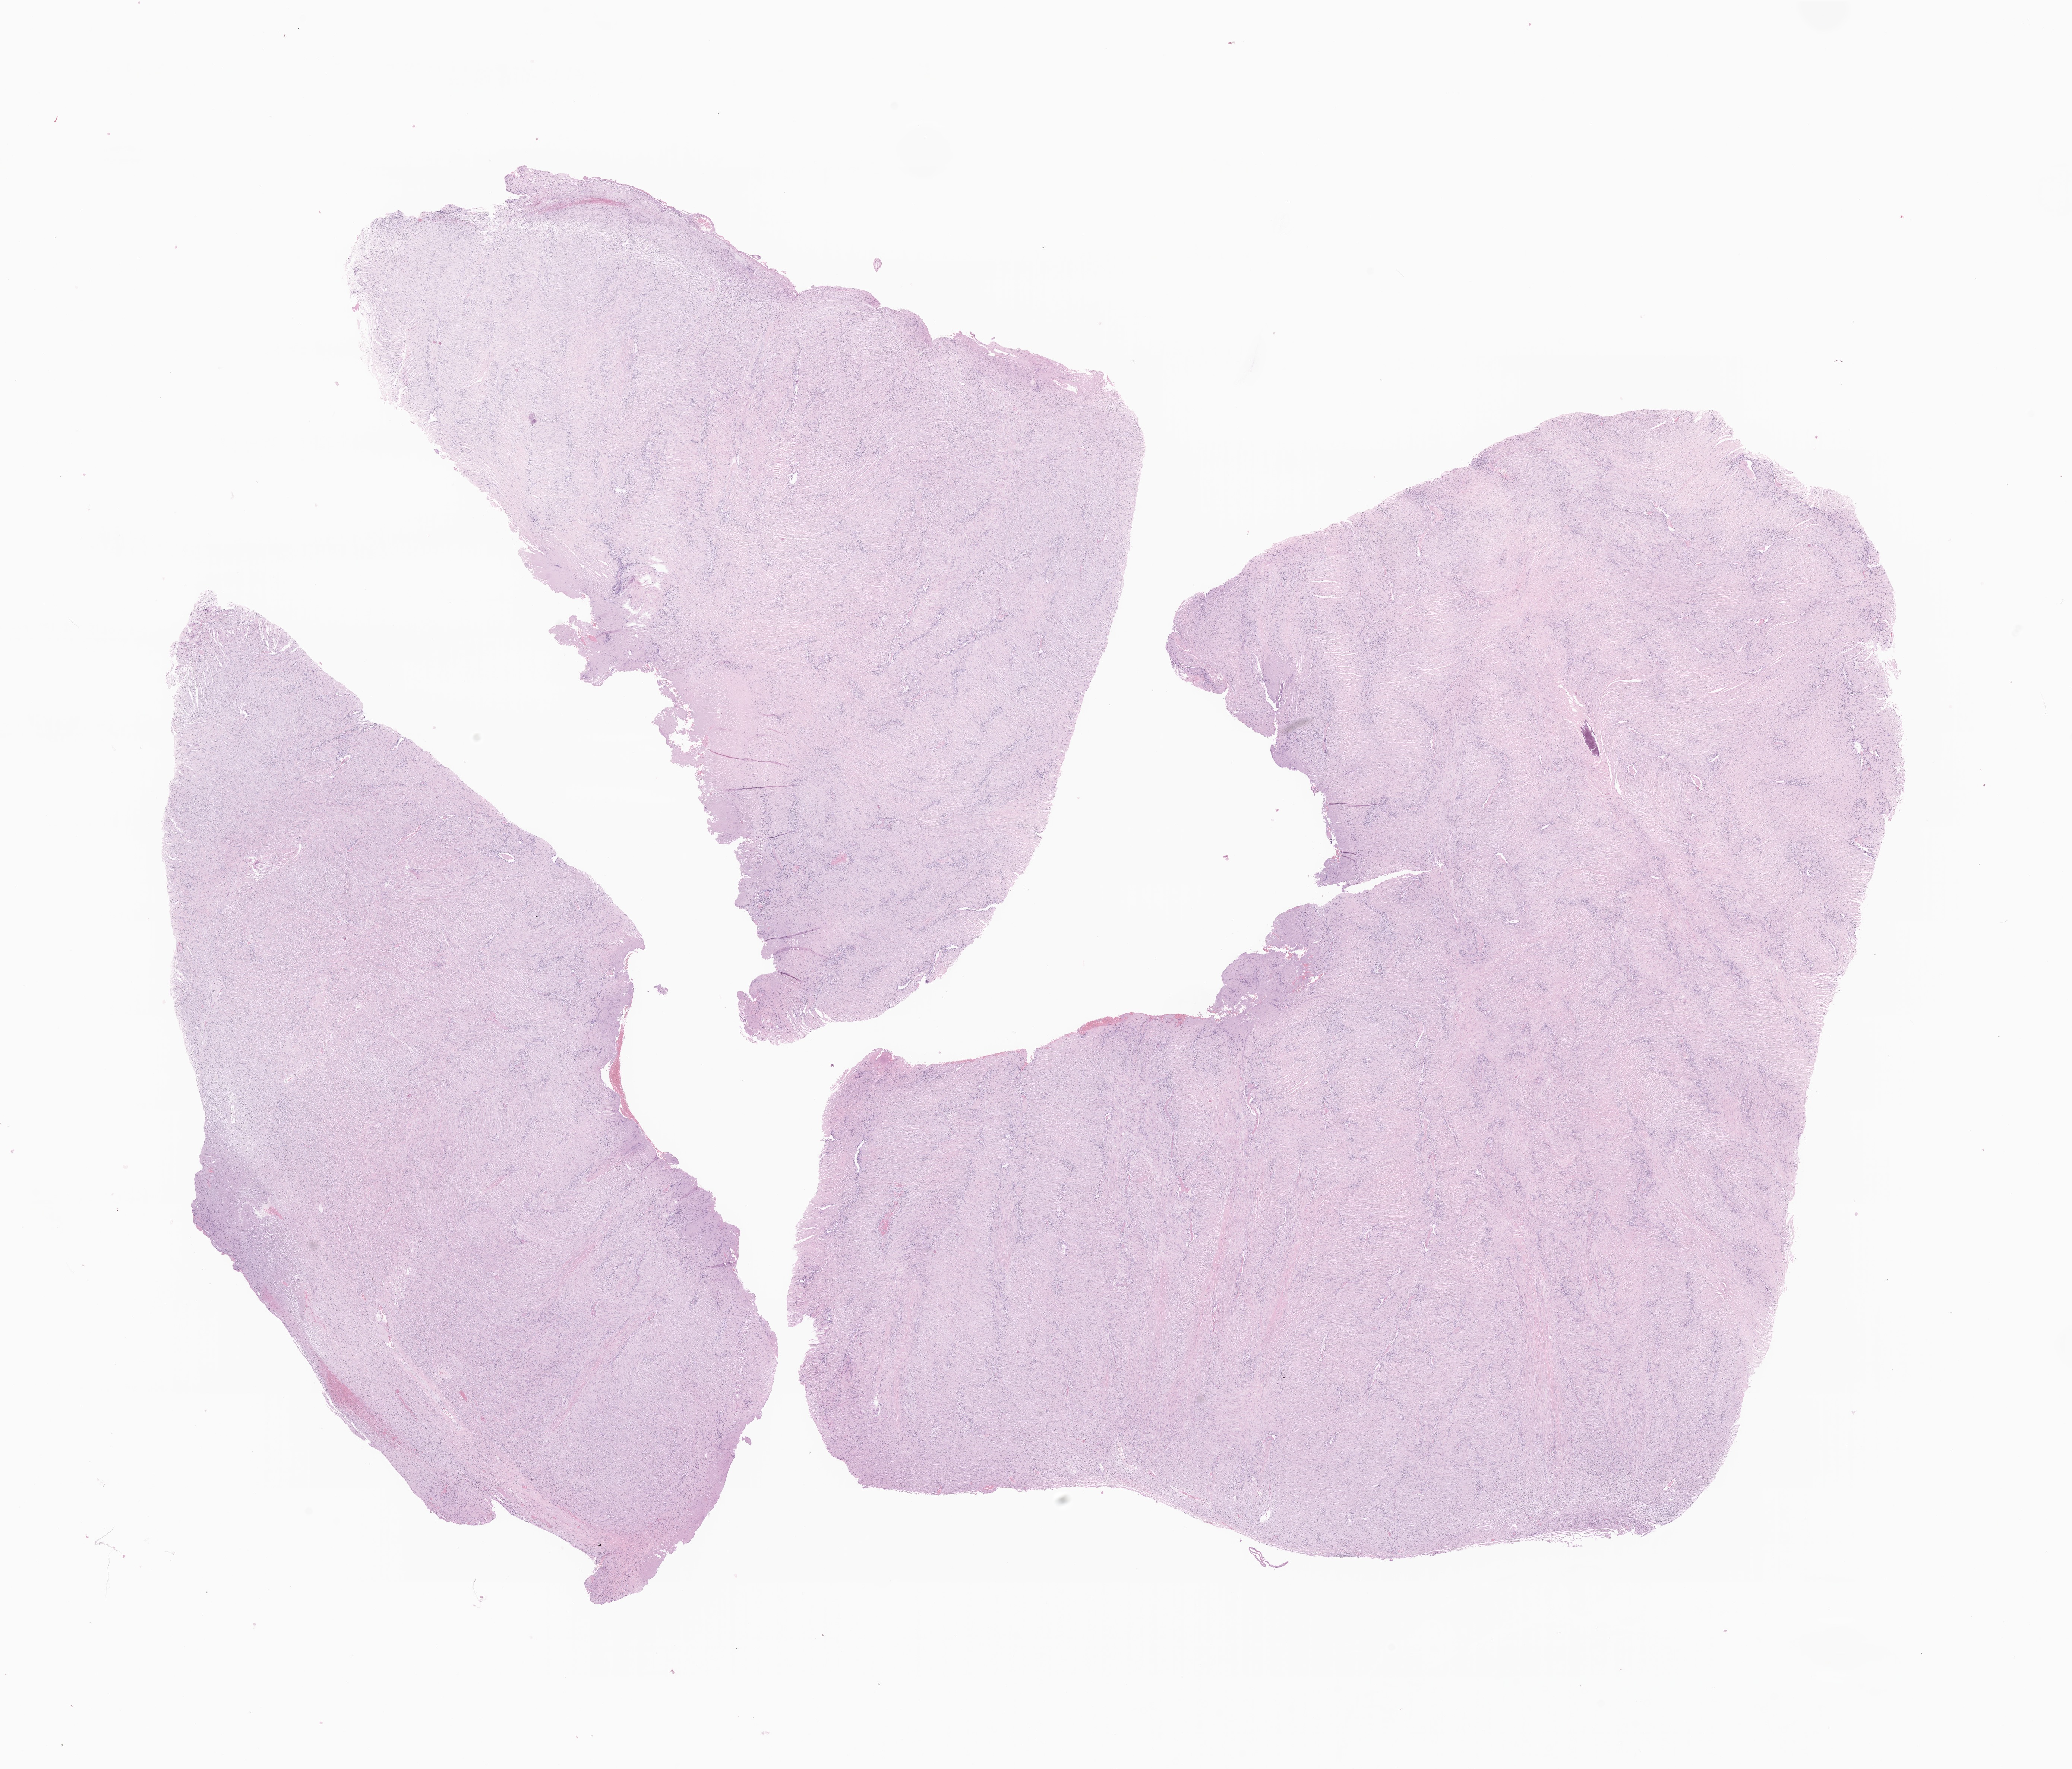
Digitized H&E-stained section of tumor tissue from the brain, shown as a low-resolution overview of the whole scanned area (about 23.4 x 20.0 mm), formalin-fixed, paraffin-embedded (FFPE) tissue. Patient female; age 206 months (17 years 2 months).
- diagnosis: Neoplasm, uncertain whether benign or malignant